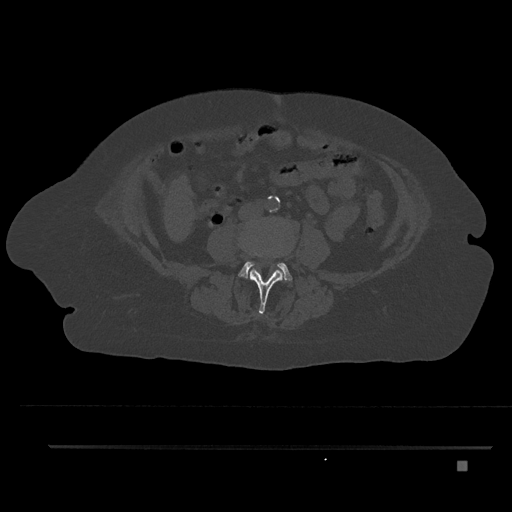
CT including the spine, one axial slice; slice 109 of 797 in the series (ordered by position); reconstruction kernel Br40s/3; 120 kVp; bone window (W 1800 / L 400 HU); 0.5 mm slice thickness; 512 × 512 image matrix, field of view 437 × 437 mm. Female patient, age 76 years. Case-level facts recorded for this patient, not image findings: primary cancer: lung; vertebrae with lytic lesions (as recorded): T11, L3.
Structures marked on this image (semi-automatic segmentation, software-assisted and operator-edited):
- L3 vertebra: bounding box [x1, y1, x2, y2] px = [245, 244, 284, 314]
- L4 vertebra: [240, 261, 292, 281]